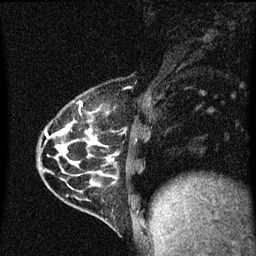
Breast MRI (dynamic contrast-enhanced), one sagittal slice; position 18 of 60 along the scan axis; dynamic contrast-enhanced series, image 2 of 3 at this slice position (ordered by acquisition); 1.5 T; TE 4.2 ms, TR 8.4 ms; 2 mm slice thickness; 256 × 256 image matrix, field of view 200 × 200 mm. Patient: female, 32 years.
Outlined on this slice (semi-automatically segmented with operator editing):
- analysis volume of interest (the breast-tissue region the enhancement analysis was run in; not a lesion): bounding box <39,92,150,169> (left, top, right, bottom; pixels)
- tumour enhancement mask (voxels above the 70 % enhancement threshold inside the analysis volume of interest): <46,132,50,139>